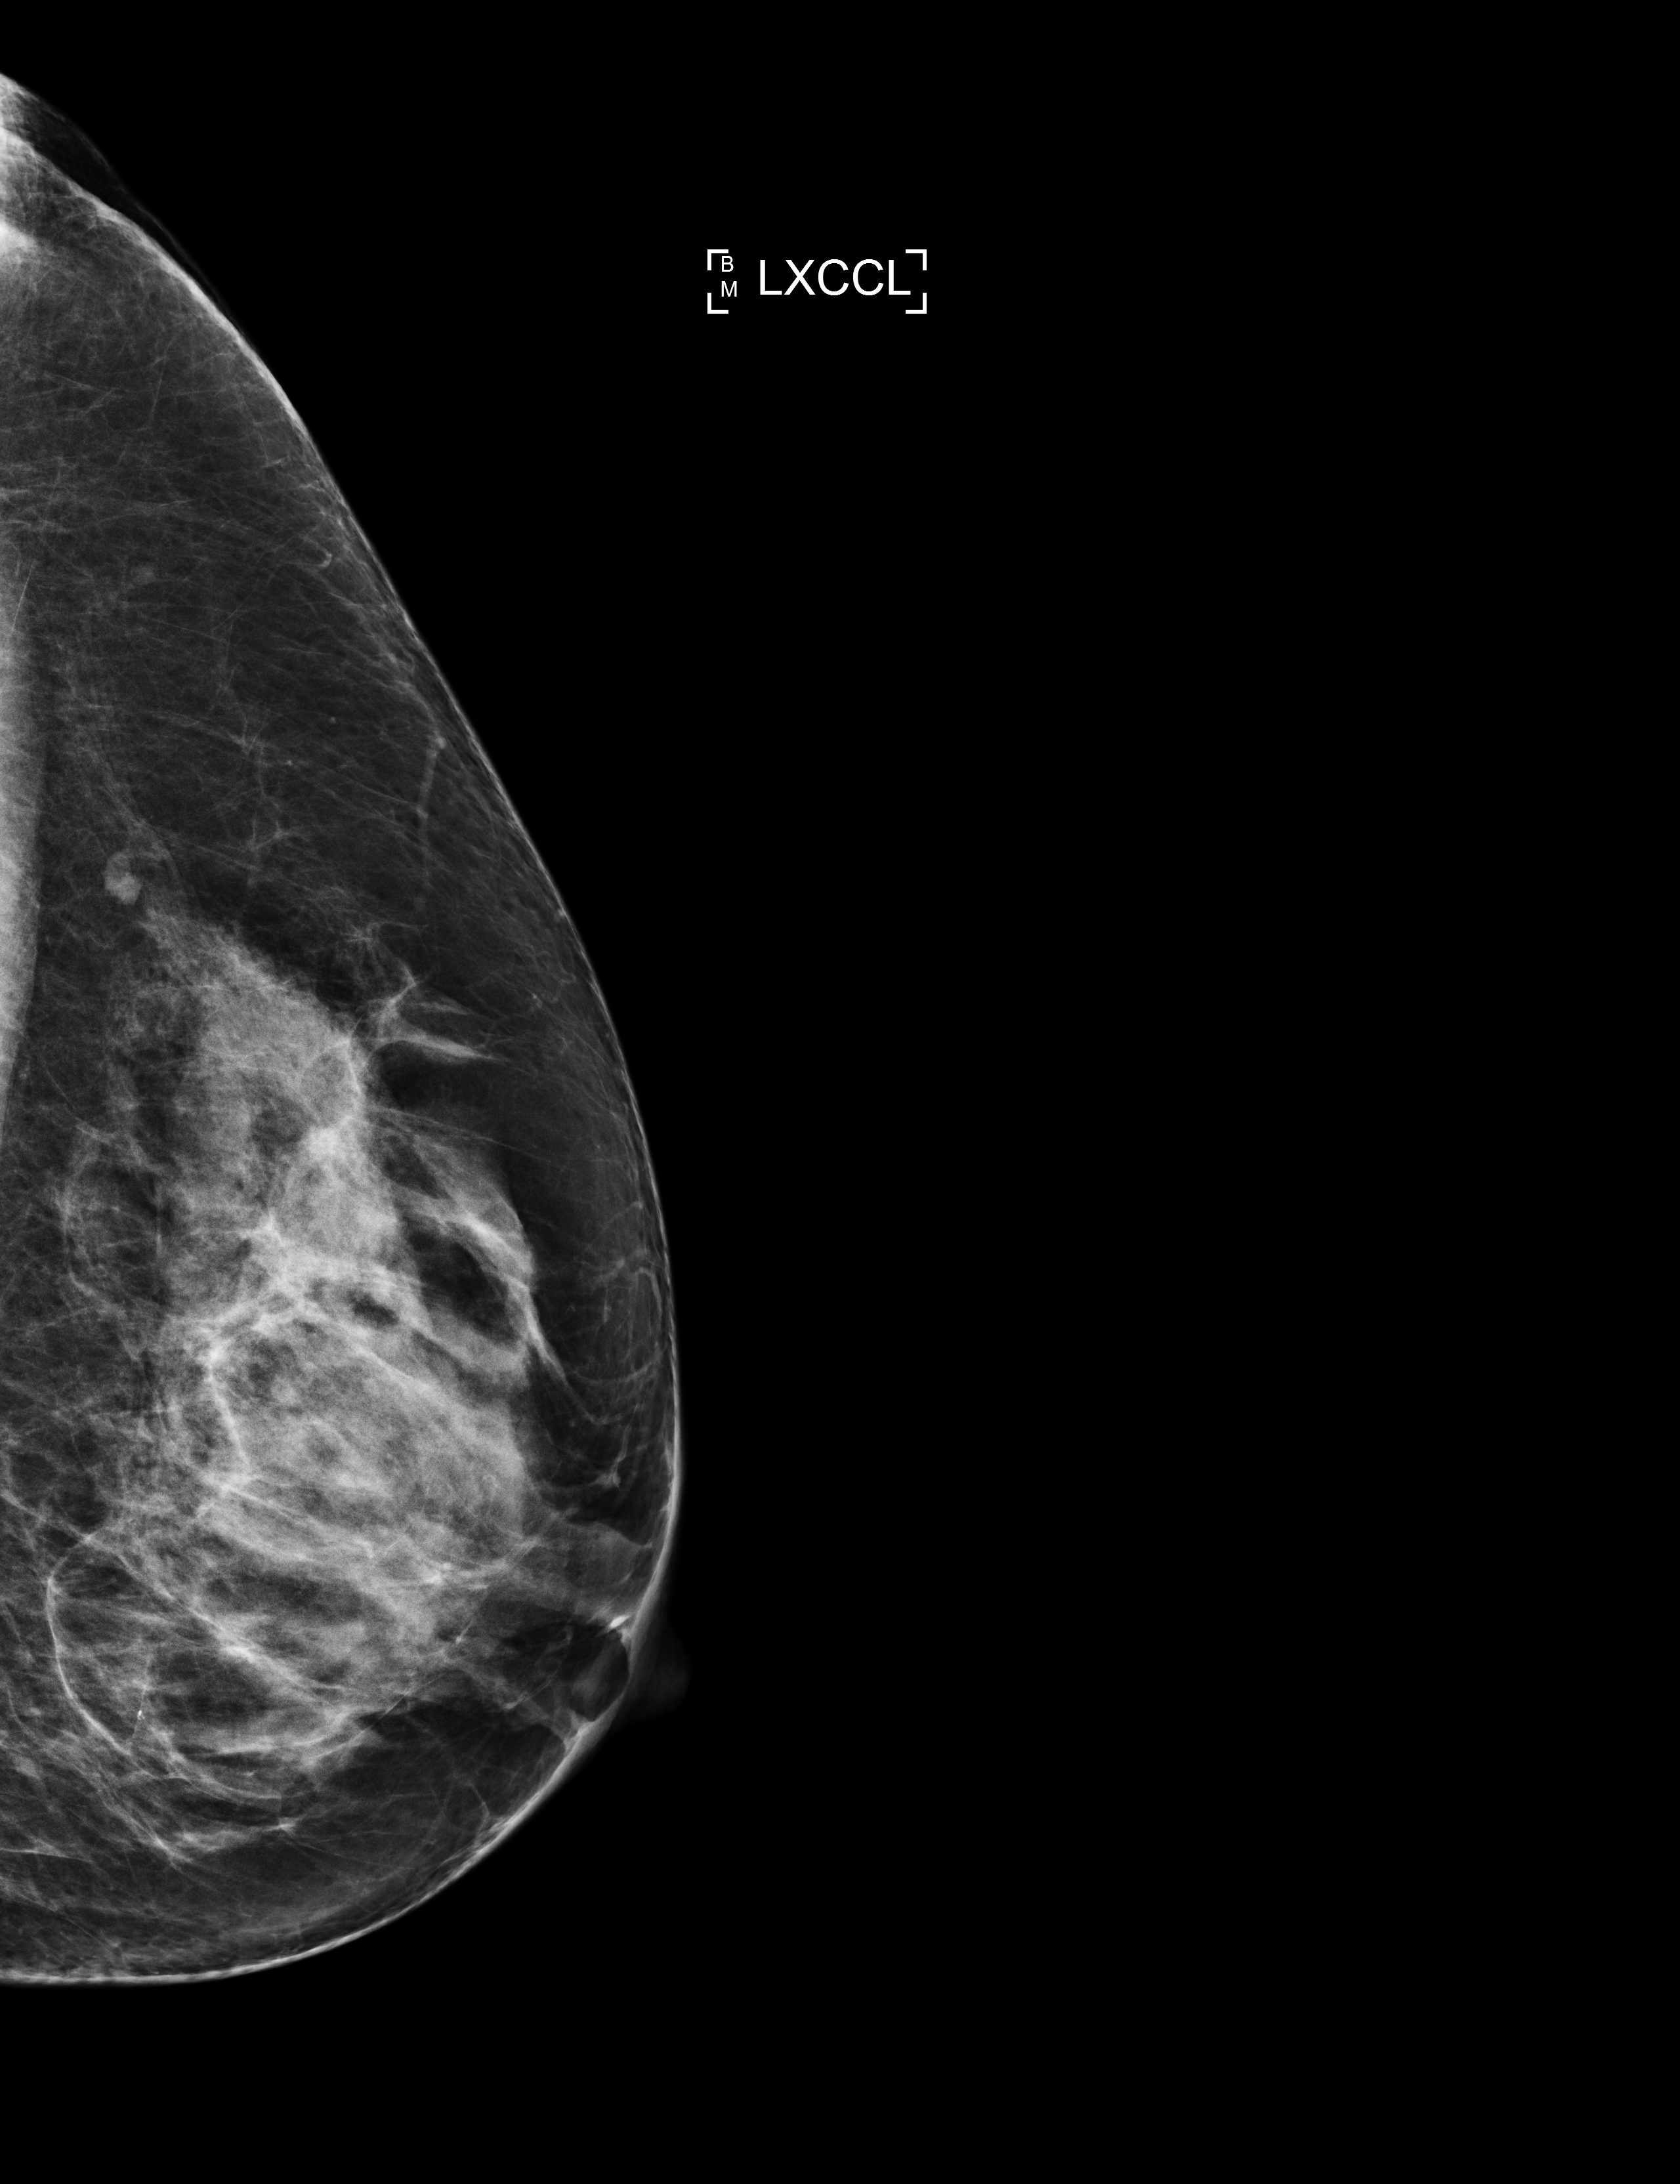
Screening examination, compressed breast thickness 58 mm, system: Selenia Dimensions. Patient: female, 60 years.
Image type: full-field digital mammogram. Breast: left. Projection: exaggerated CC view (lateral).